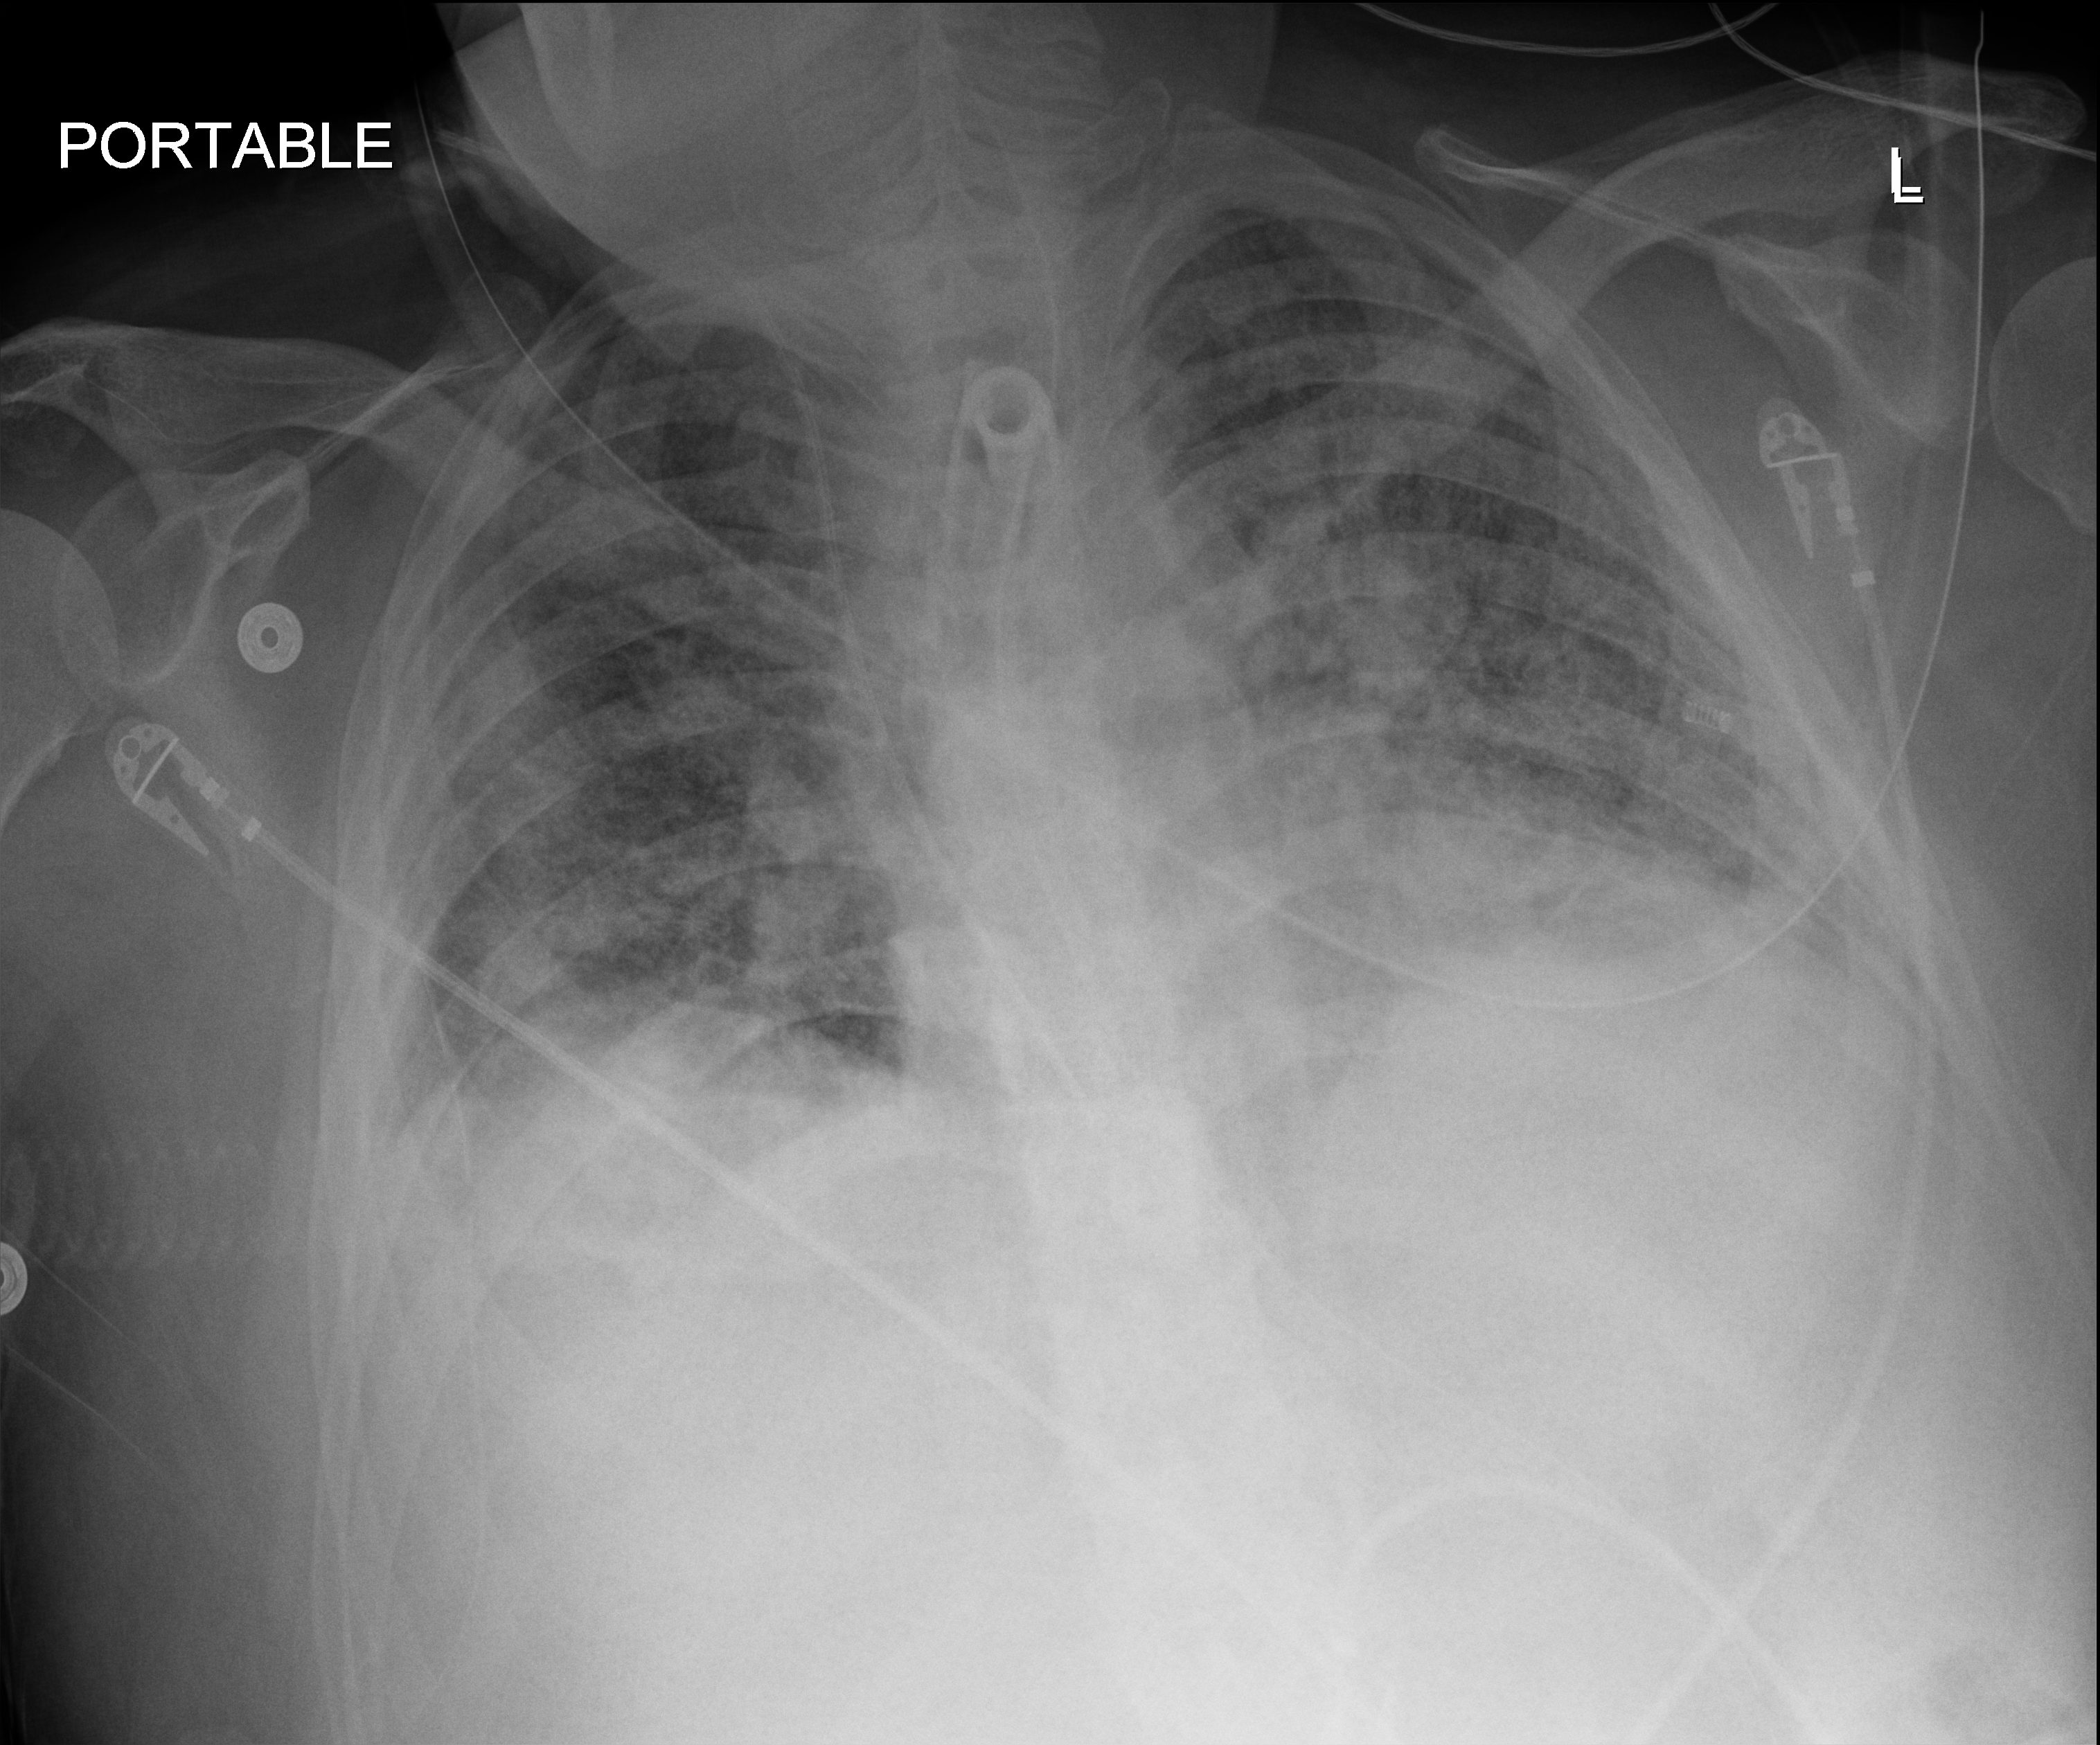
Portable chest radiograph. Patient hospitalised with COVID-19; male, aged 18–59 years.
Hospital-stay facts (about this admission, not read from this image; timing relative to this image not recorded):
- mechanically ventilated during this hospital stay: yes
- admitted to intensive care during this hospital stay: yes